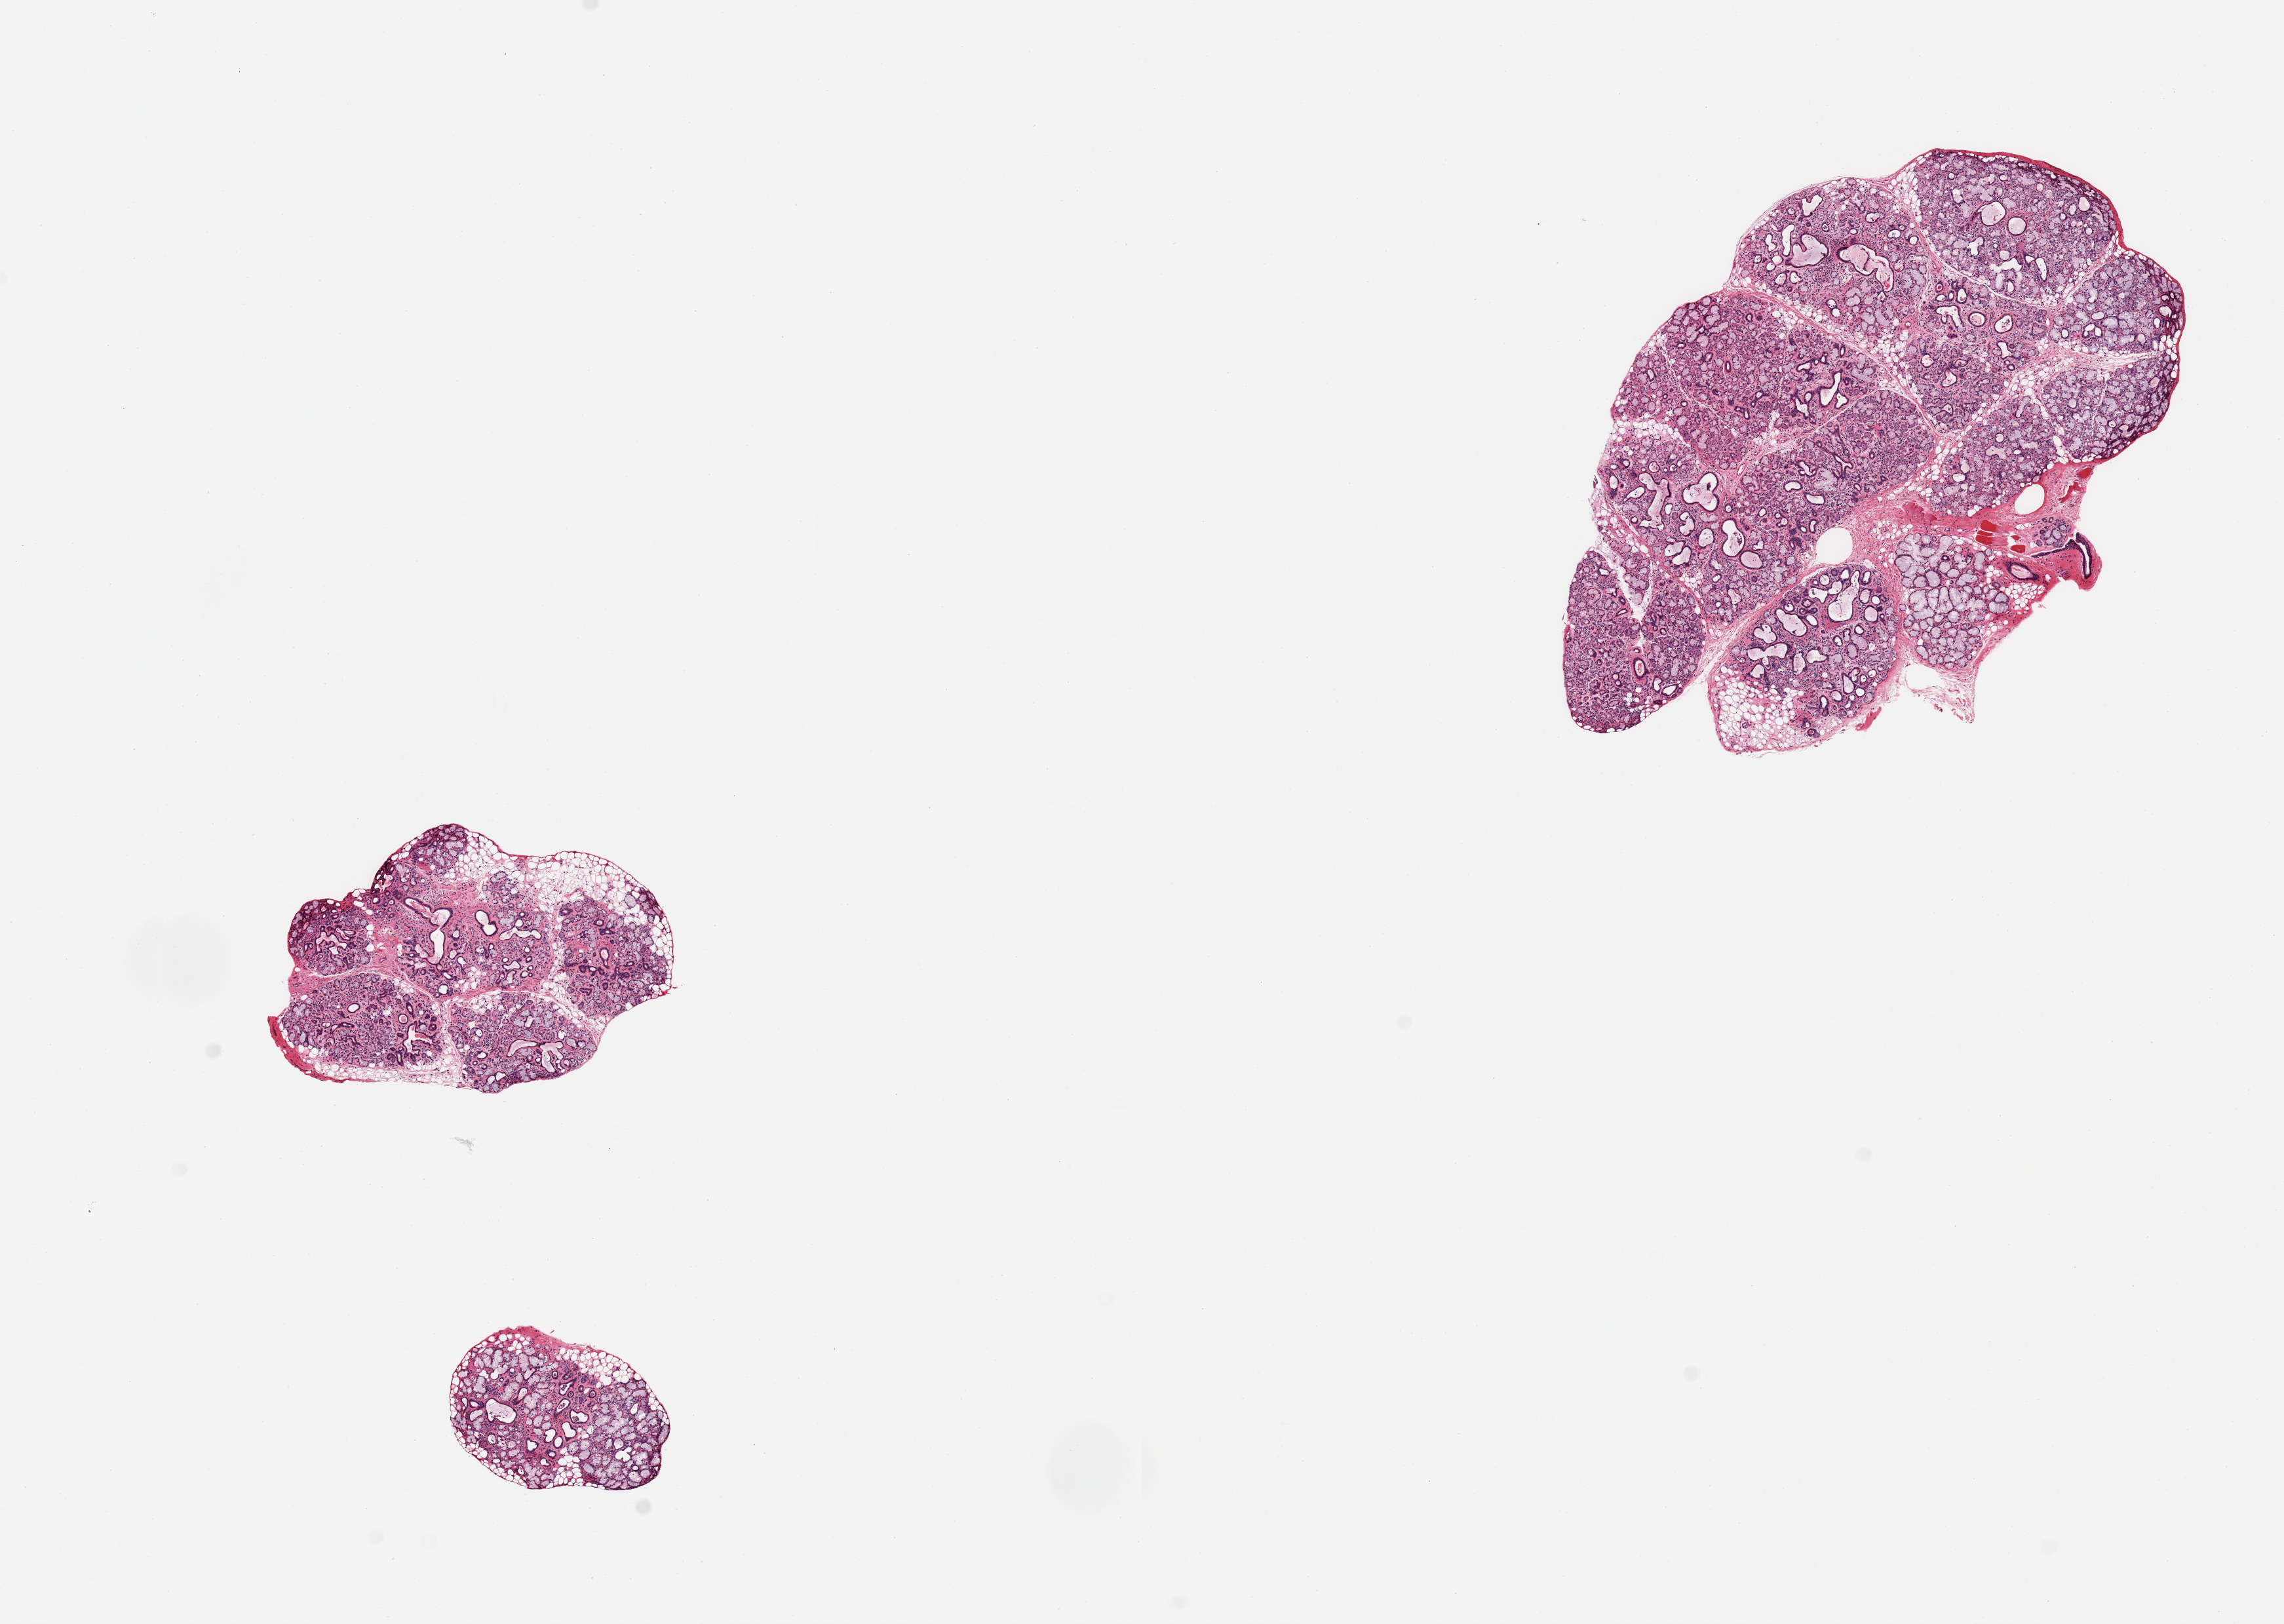
Digitized hematoxylin and eosin (H&E)-stained section — a low-resolution overview of the entire scanned area, about 13.8 x 9.8 mm (from a 20x scan); PAXgene-fixed, paraffin-embedded tissue; section of minor salivary gland (target tissue); tissue donor sample.
Reviewer comment on this tissue sample: 3 pieces; well dissected glands; focal atrophy with ductal dilatation; small focus of skeletal muscle.